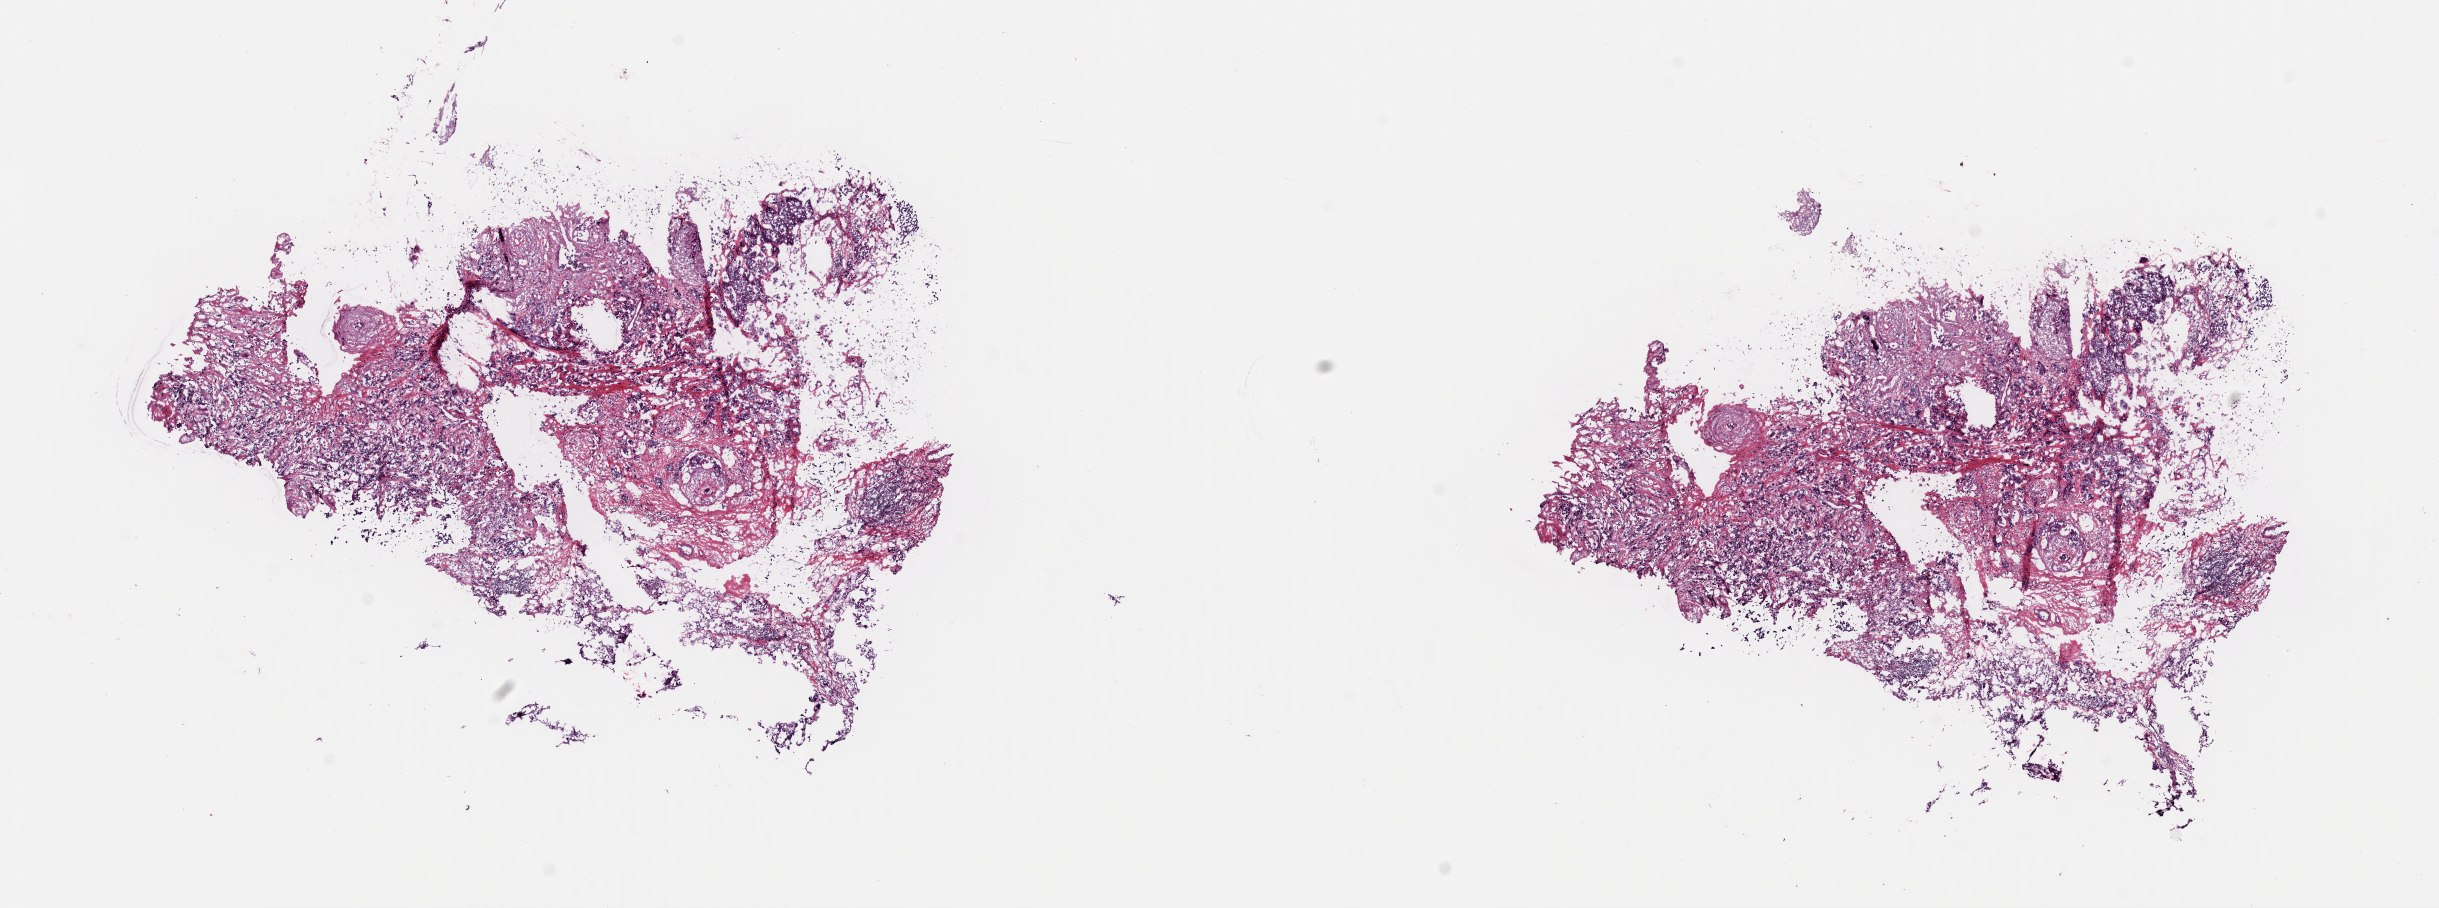
Digitized Hematoxylin and eosin (H&E) stained tissue section (whole slide), shown as a low-resolution overview of the whole scanned area (about 19.3 x 7.2 mm, slide scanned at 40x). Frozen section from the top of the tissue portion. Sample: primary tumour, breast. Patient: female, age at initial diagnosis 70 years. Composition of this section per pathologist review: tumour cells 55%, tumour nuclei 75%, normal cells 0%, stromal cells 43%, necrosis 2%. Infiltration values recorded for this section: lymphocyte infiltration 5%, monocyte infiltration 0%, neutrophil infiltration 0%.
• lymph nodes positive (case pathology): 0 of 4 examined
• pathologic diagnosis: Lobular carcinoma, NOS
• AJCC pathologic stage: IIB (6th edition)